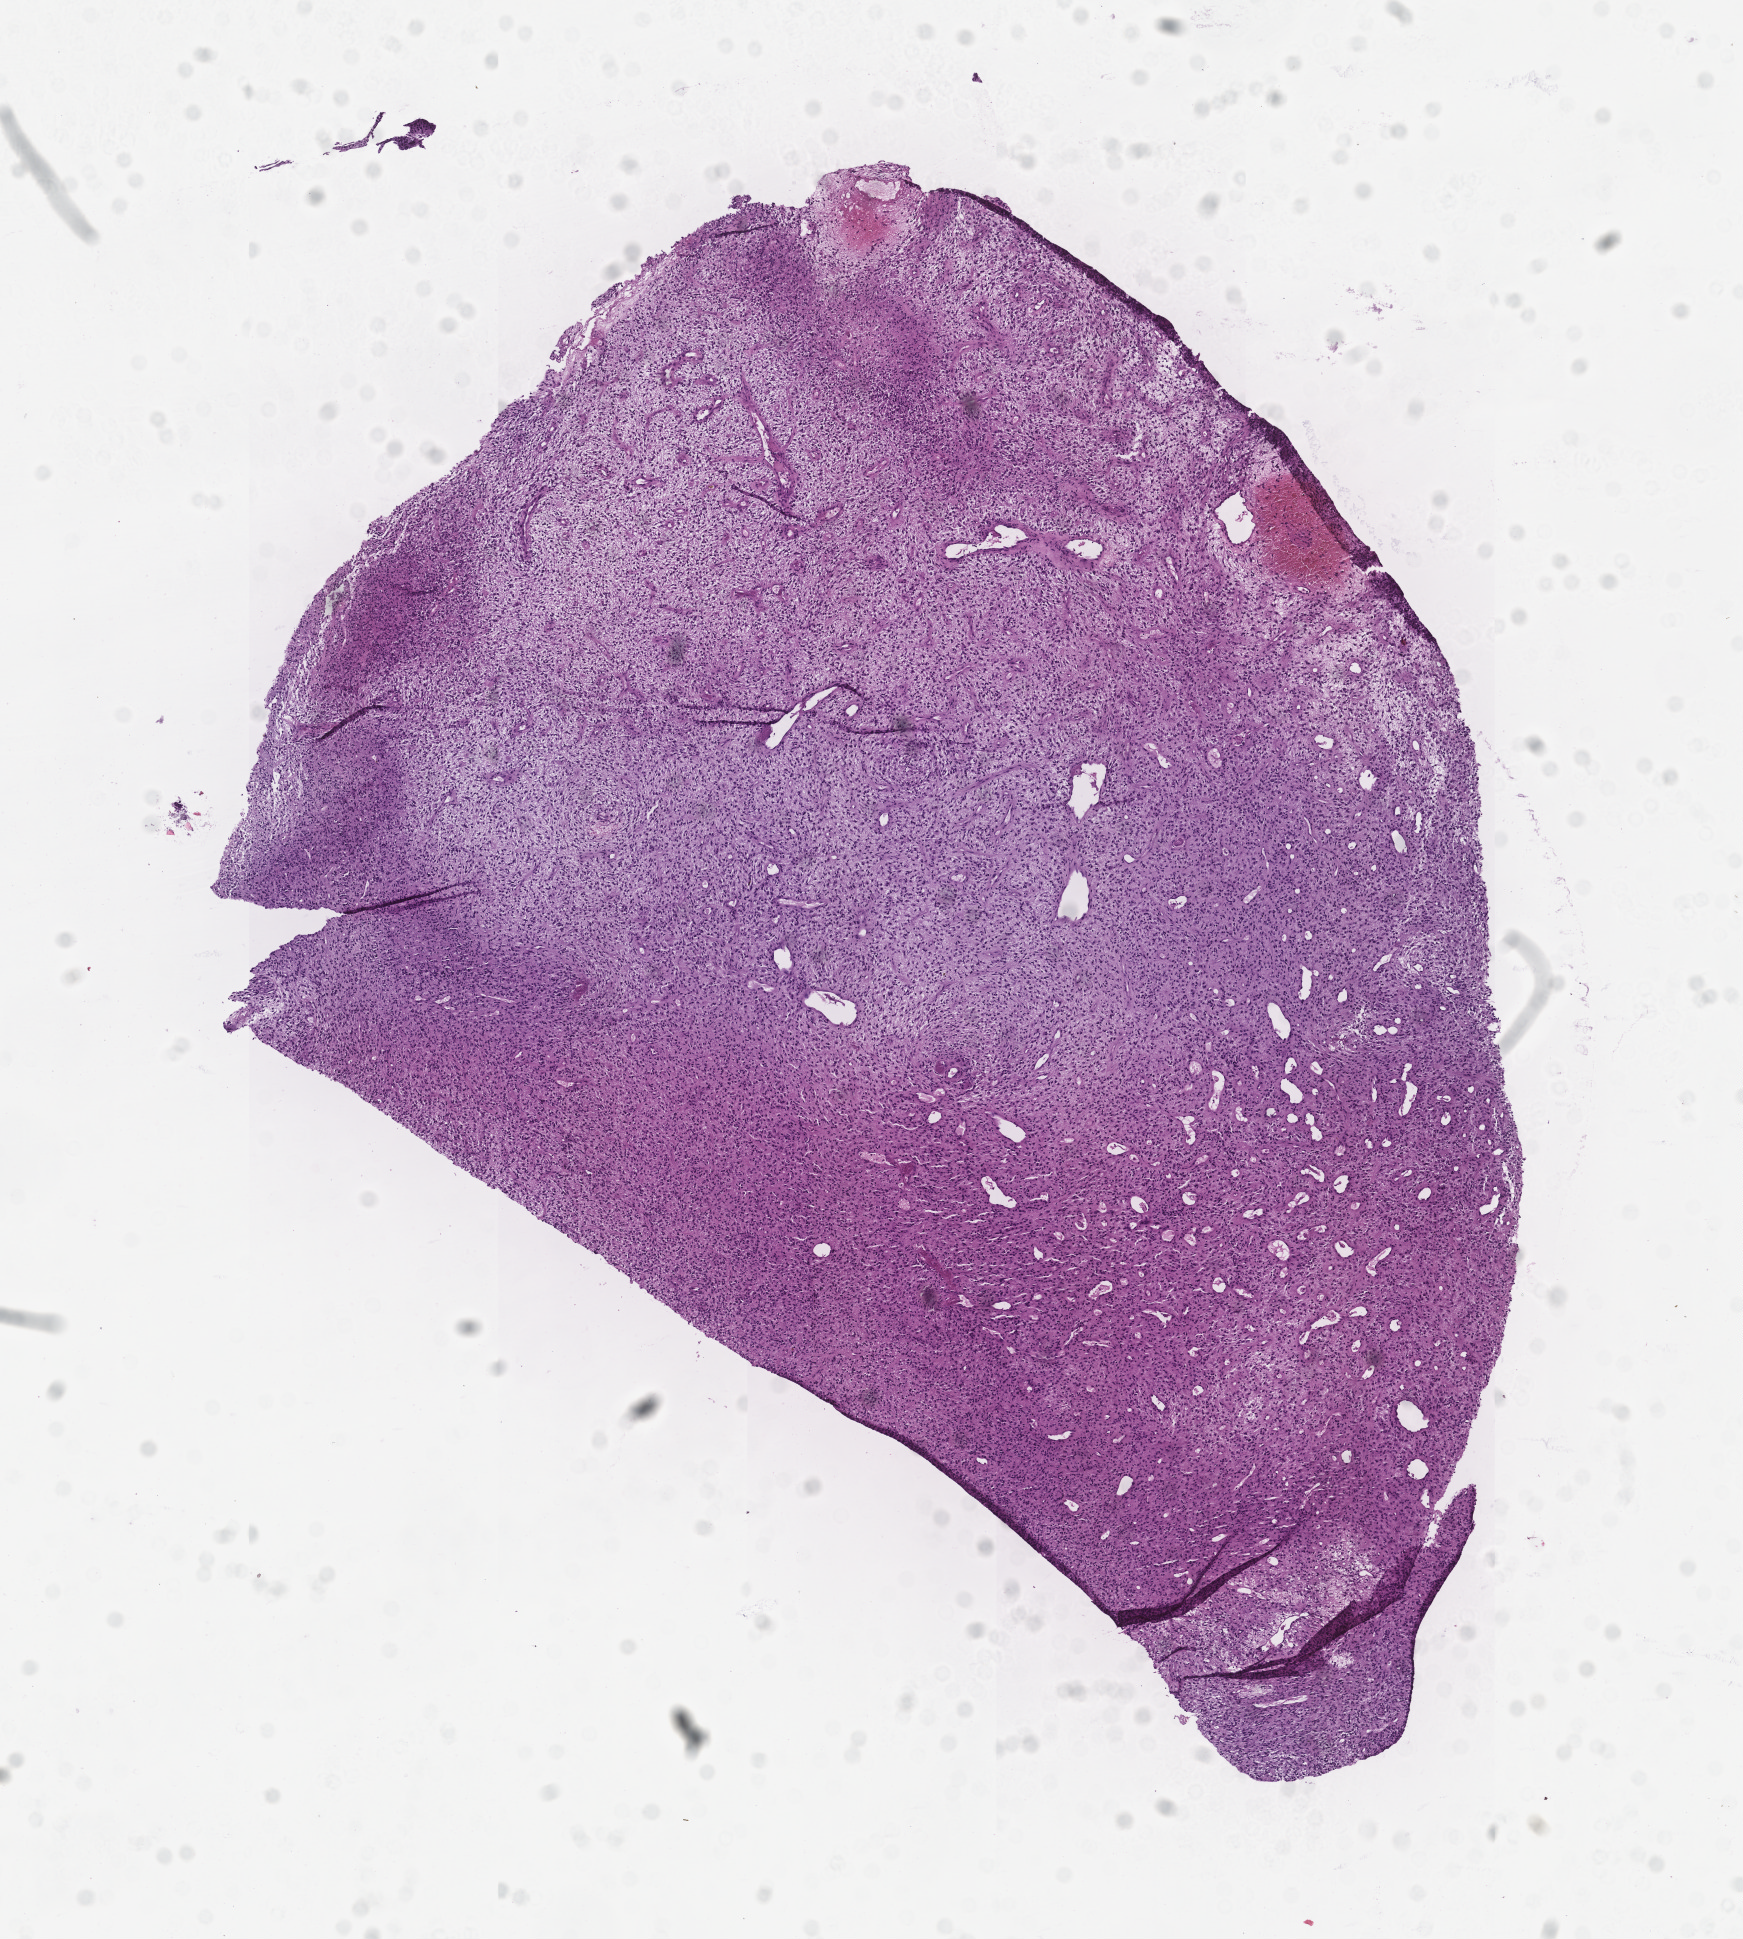
H&E whole-slide image — low-resolution overview of the scanned area, about 7.0 x 7.8 mm (acquisition: 20x scan); brain, tumour tissue. Patient: female, age 51 years.
- histologic diagnosis: Glioblastoma